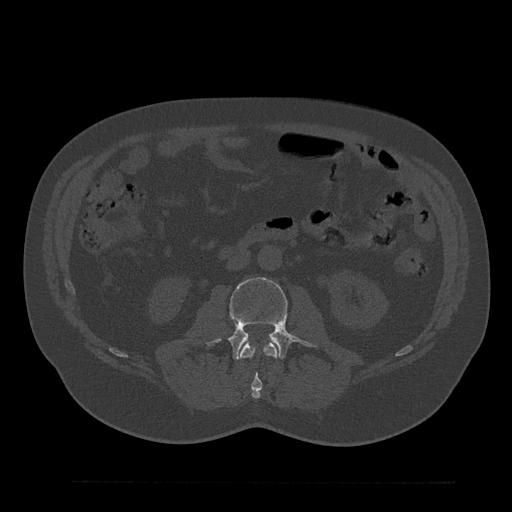
CT including the spine, one axial slice. Slice 57 of 797 in the series (ordered by position). Reconstruction kernel Br40s/3. 120 kVp. Bone window (W 1800 / L 400 HU). 0.5 mm slice thickness. 512 × 512 image matrix. Patient: male, 61 years. Case-level facts recorded for this patient, not image findings: primary cancer: prostate.
Outlined on this slice (semi-automatic segmentation, software-assisted and operator-edited):
- L2 vertebra: bounding box <239,342,278,399> (left, top, right, bottom; pixels)
- L3 vertebra: <229,277,311,359>